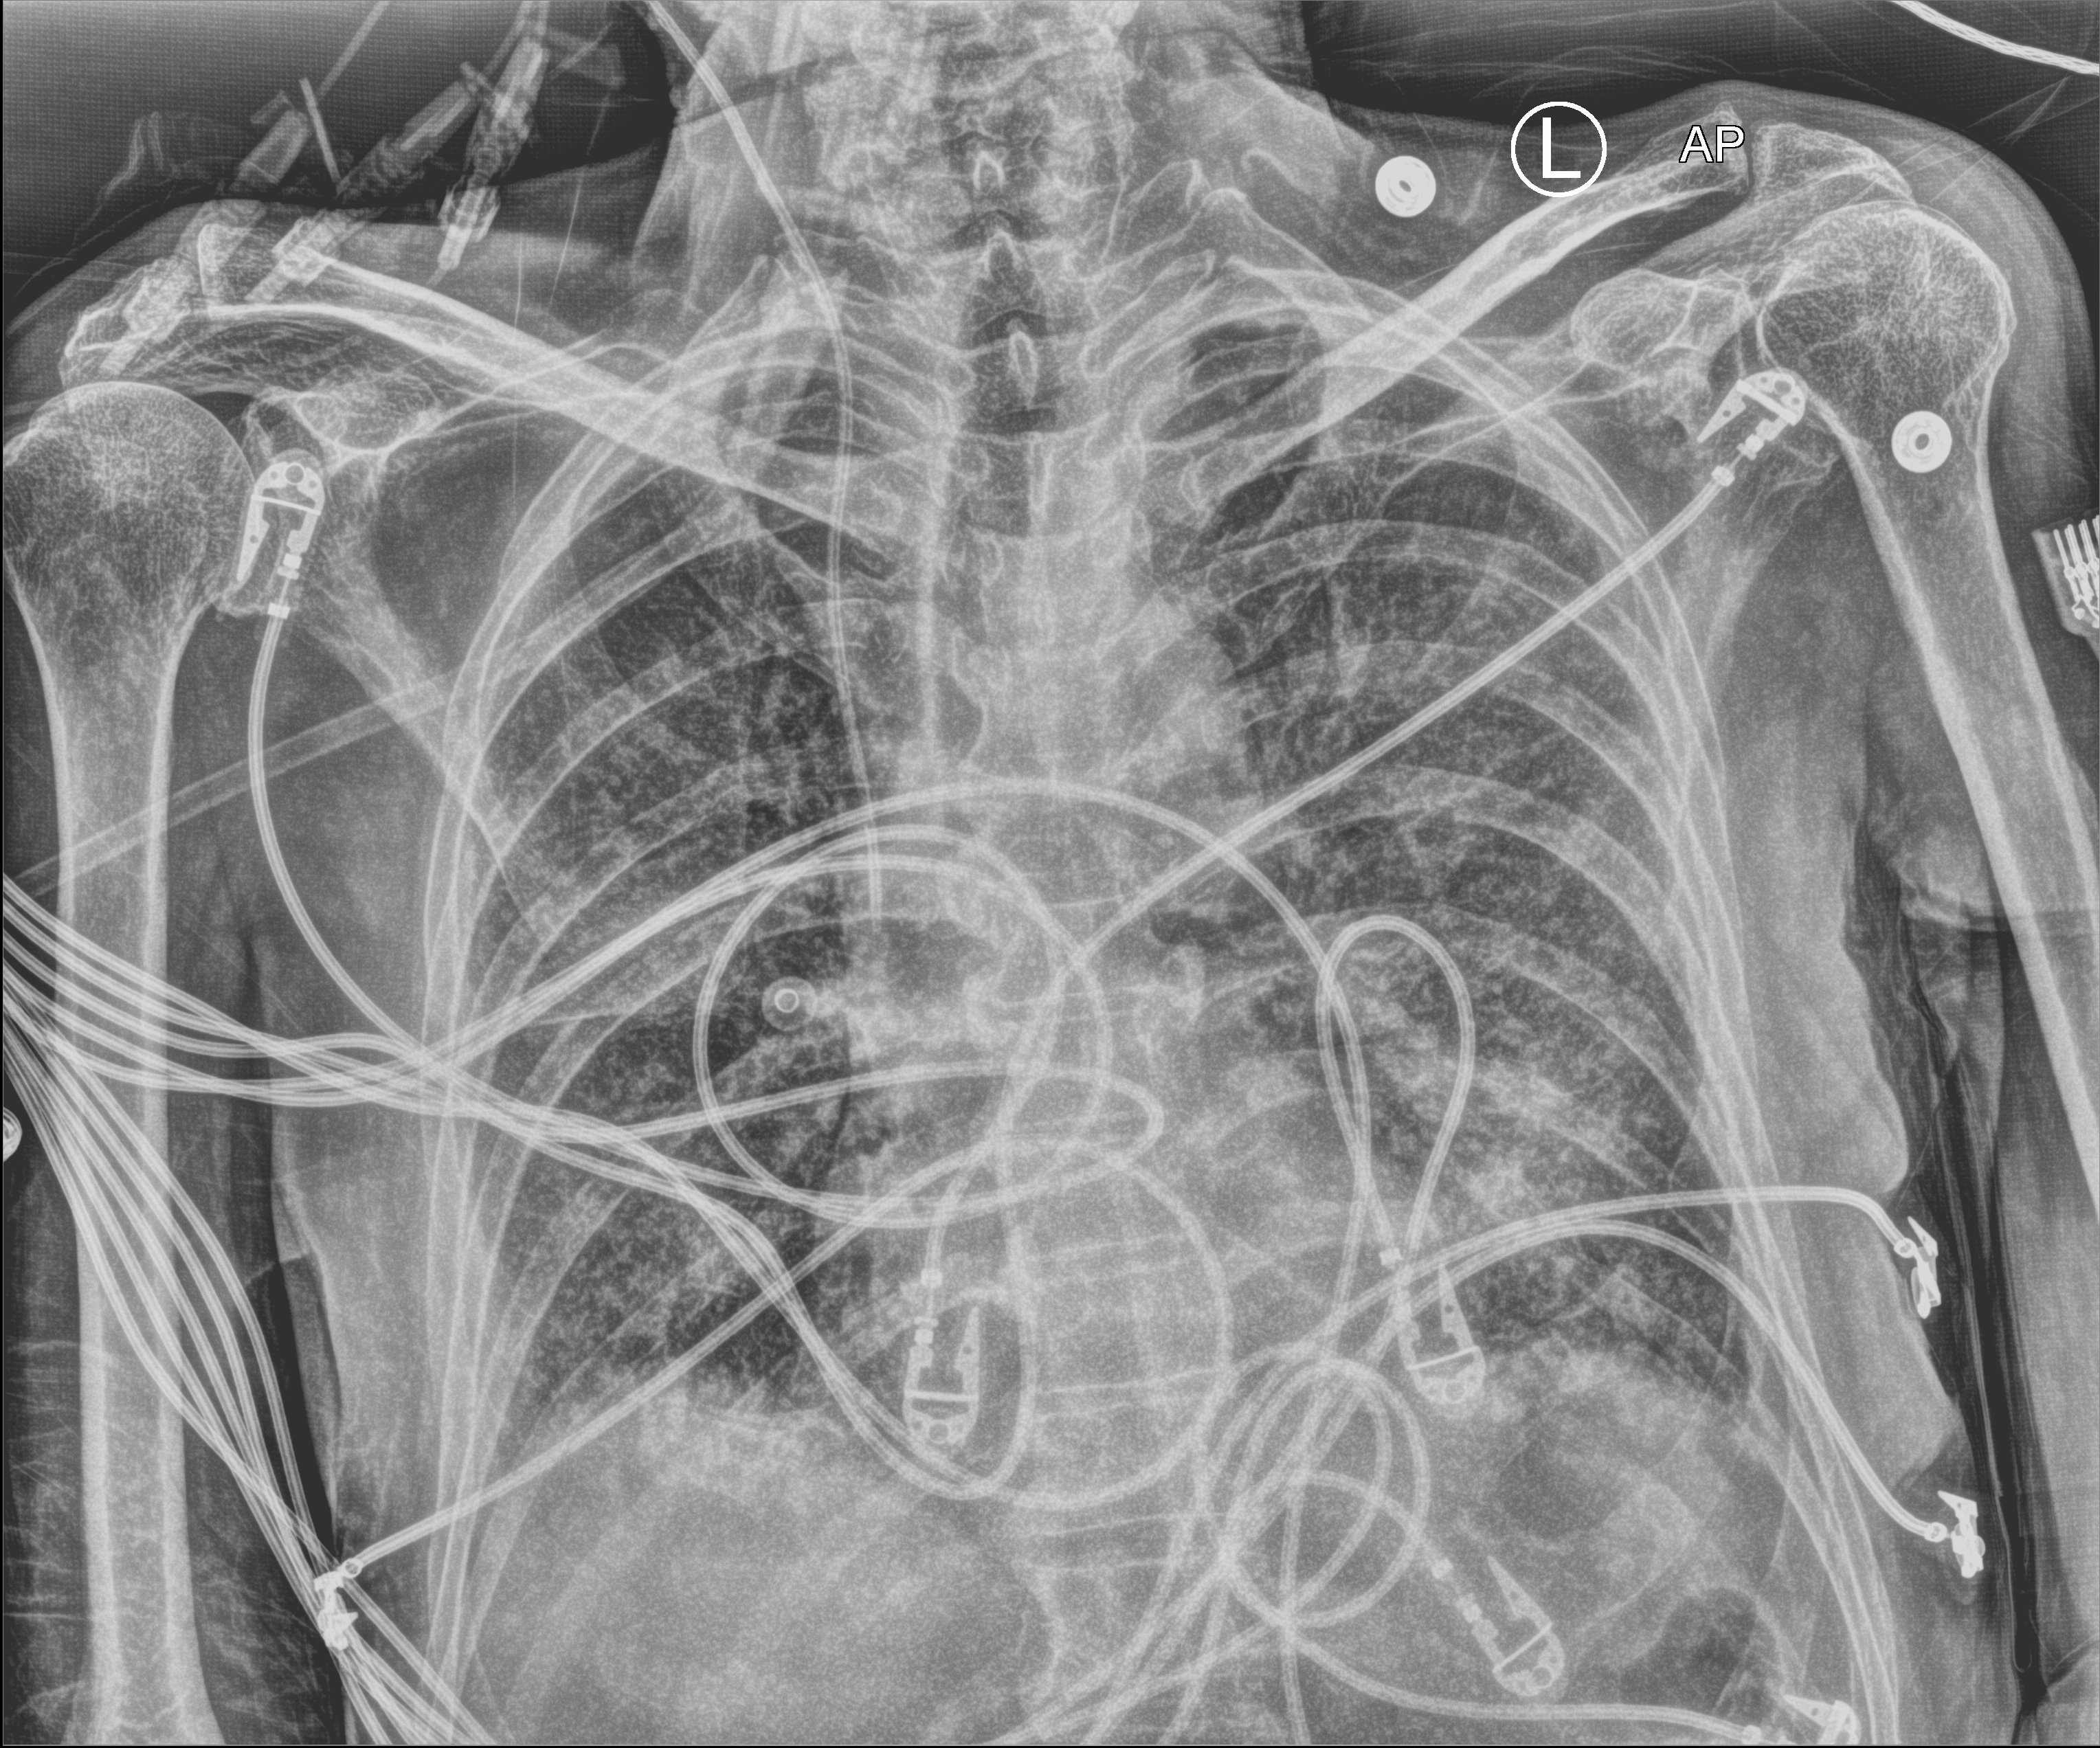
Bedside chest radiograph (computed radiography). Patient hospitalised with COVID-19; male, aged 60–74 years.
Hospital-stay facts (about this admission, not read from this image; timing relative to this image not recorded): mechanically ventilated during this hospital stay: yes; COPD (admission record): no; admitted to intensive care during this hospital stay: yes.